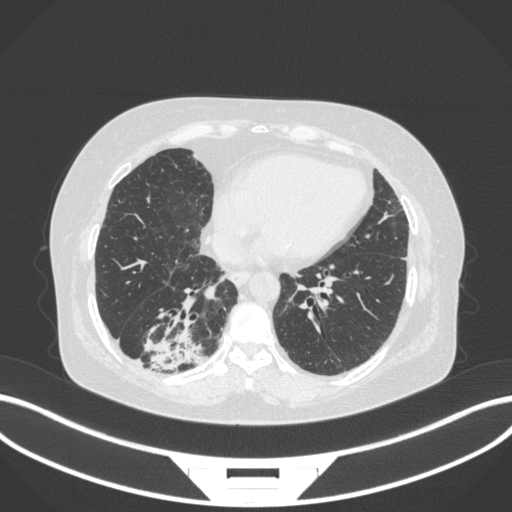
Chest CT, one axial slice; slice 76 of 303 in the series (ordered by position); reconstruction kernel B31f; lung window (W 1500 / L -600 HU); 1 mm slice thickness; 512 × 512 image matrix, field of view 400 × 400 mm. Female patient, age 65 years. From the clinical record (not read from this slice): clinical TNM (as recorded): T2b N1 M0; histopathological grade: G1.
Structures marked on this image (bounding box drawn by a radiologist):
- lung tumour (recorded histology: adenocarcinoma): bounding box [x1, y1, x2, y2] px = [140, 305, 207, 370]